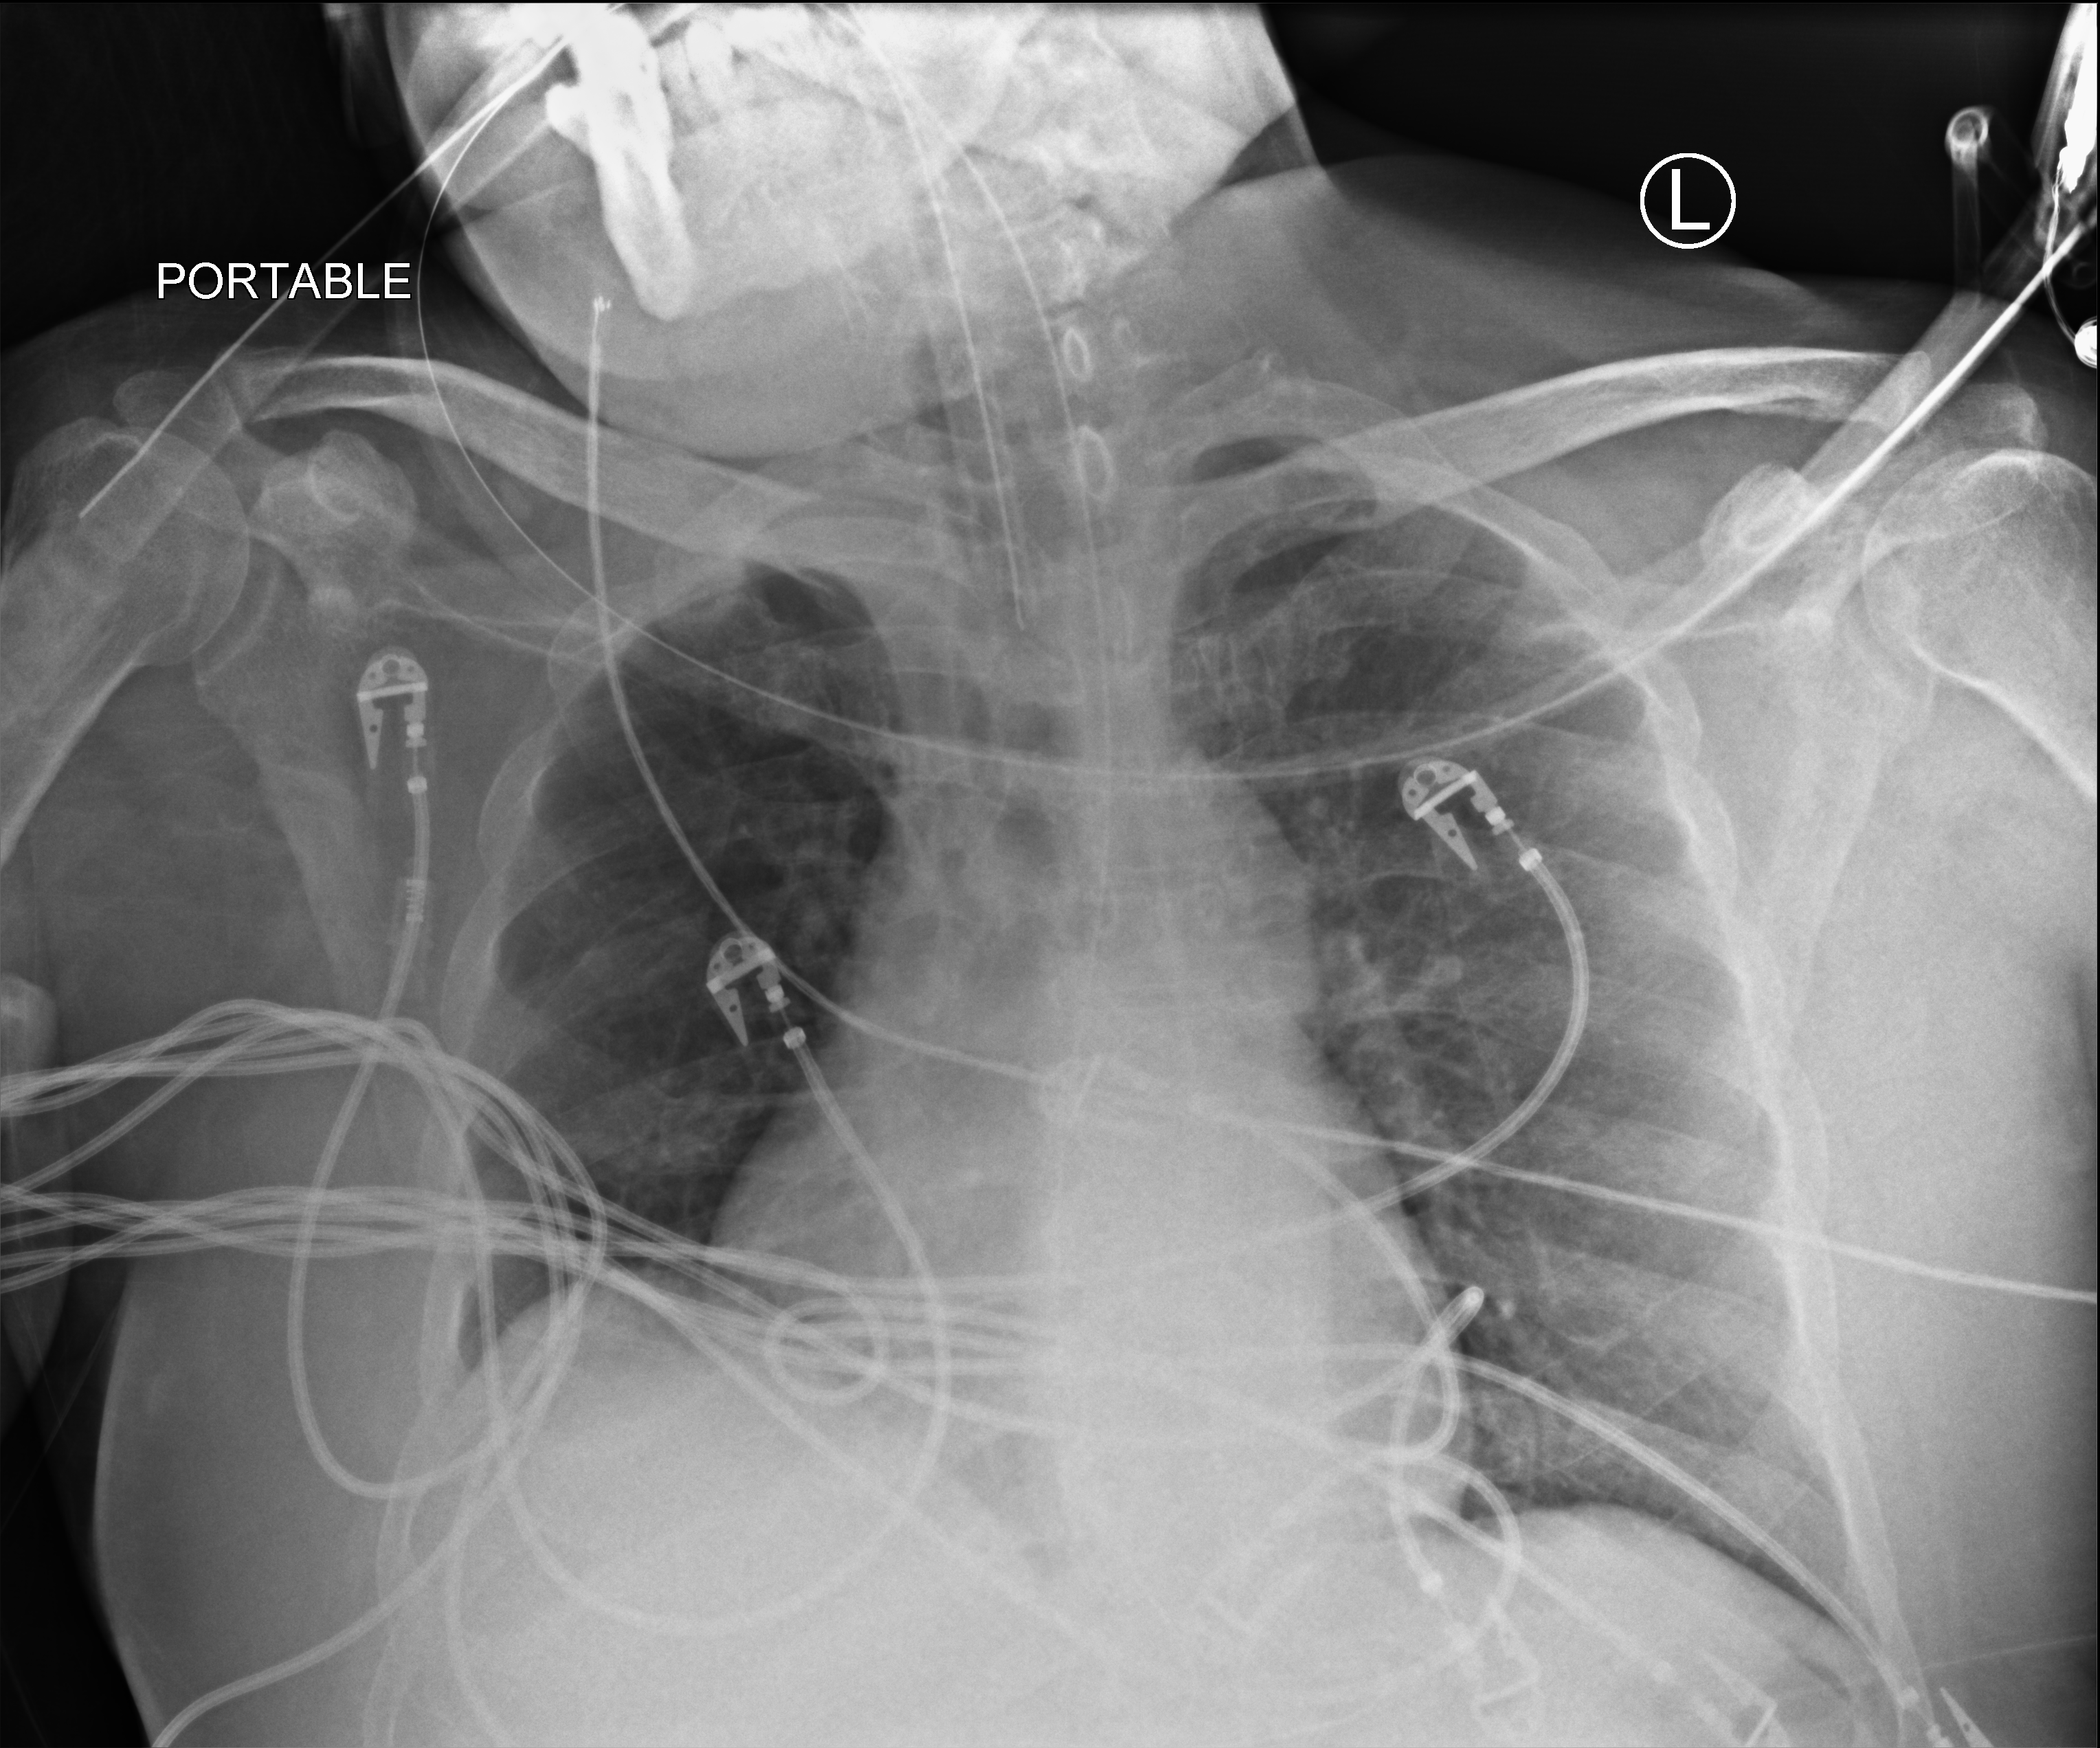
Bedside chest radiograph (computed radiography); anteroposterior (AP) projection. Patient hospitalised with COVID-19, aged 18–59 years.
Admission-level facts for this patient (not findings on this image; timing relative to this image not recorded):
- chronic kidney disease (admission record): no